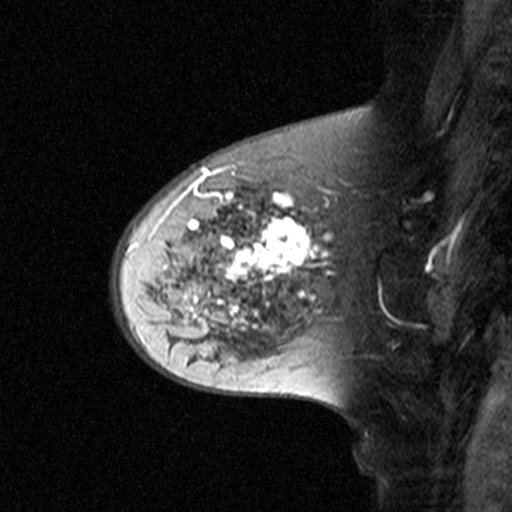
Breast MRI (dynamic contrast-enhanced), one sagittal slice. Slice 29 of 44 in the series (ordered by position). Dynamic contrast-enhanced study with each time point stored as its own series, time point 2 of 3 at this slice position (early post-contrast, ordered by acquisition time). 1.5 T. TE 4.5 ms, TR 11 ms. 3 mm slice thickness. 512 × 512 image matrix, field of view 200 × 200 mm. Female patient, age 65 years. Case-level facts recorded for this patient, not image findings: setting: breast cancer imaged before/during neoadjuvant chemotherapy; receptor status: HER2-positive.
Outlined on this slice (semi-automatically segmented with operator editing):
- analysis volume of interest (the breast-tissue region the enhancement analysis was run in; not a lesion): box from (x=160, y=172) to (x=329, y=345) px
- tumour enhancement mask (voxels above the 90 % enhancement threshold inside the analysis volume of interest): (x=167, y=172)–(x=329, y=331)